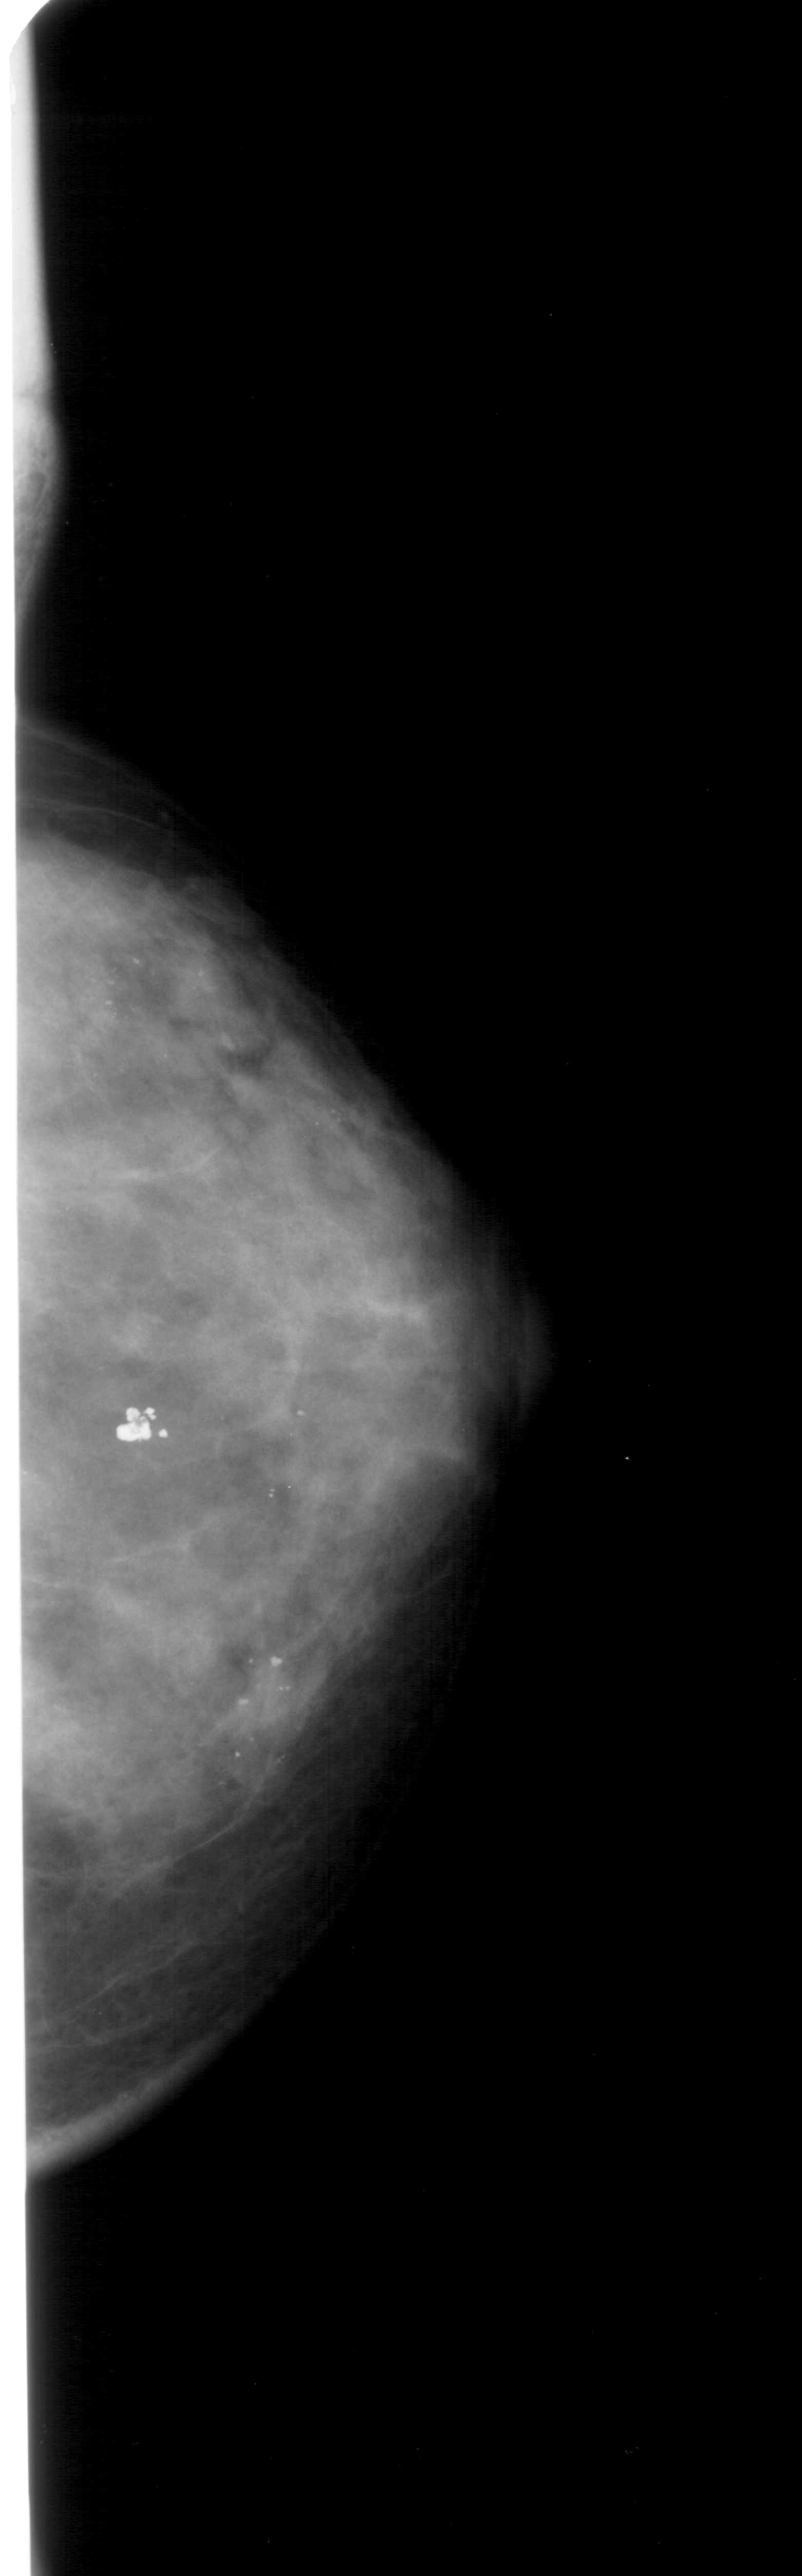
Mammogram (digitized film); right breast; CC view; breast composition: extremely dense (BI-RADS density category 4 of 4).
Finding: calcifications, morphology pleomorphic, distribution clustered; BI-RADS assessment category 4; pathology result (as recorded, not read from the image): malignant.